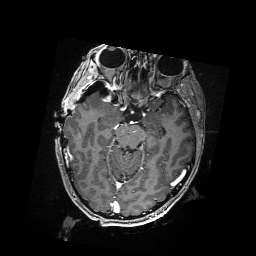
Brain MRI from a brain-tumour surgery series, one axial slice. Slice 111 of 176 in the series (ordered by position). T1-weighted post-contrast. 1 mm slice thickness. 256 × 256 image matrix, field of view 256 × 256 mm. From the clinical record (not read from this slice): histopathology: Metastatic Carcinoma from Breast primary; tumour location: Right Frontal.
Annotated regions visible in this slice (expert manual segmentation):
- residual tumour: bounding box (x1, y1, x2, y2) in pixels: (91, 88, 102, 95)